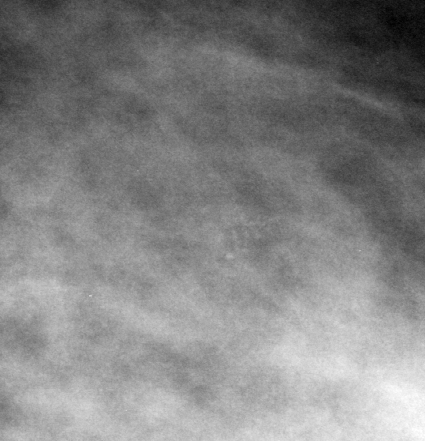
Cropped region of a digitized screen-film mammogram centred on a radiologist-marked abnormality, left breast, MLO view, BI-RADS breast density category 3 (scale 1–4).
- Marked abnormality: calcifications, morphology amorphous, distribution clustered; BI-RADS assessment category 4; pathology (as recorded): benign.